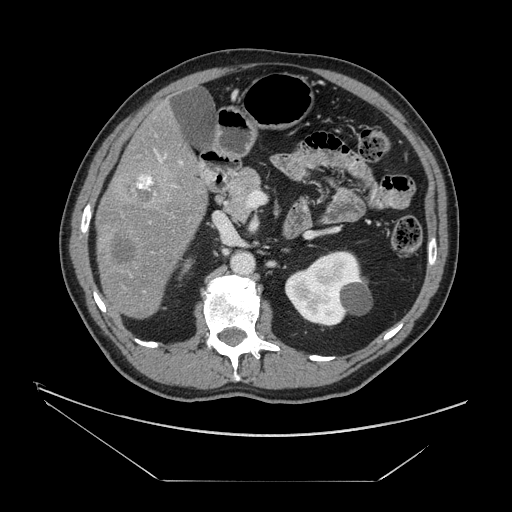
Contrast-enhanced abdominal CT, one axial slice; position 72 of 161 along the scan axis; 120 kVp; intravenous contrast given; soft-tissue window (W 400 / L 40 HU); 2.5 mm slice thickness; 512 × 512 image matrix, field of view 440 × 440 mm. Male patient, age 65 years. From the clinical record (not read from this slice): diagnosis: colorectal cancer liver metastases, imaged before liver resection; multiple liver metastases: yes; largest metastasis: 4.2 cm; chemotherapy before resection: yes.
Annotated regions visible in this slice (outlined manually by an expert reader):
- liver: box from (x=98, y=108) to (x=207, y=318) px
- portal vein (with intrahepatic branches): (x=138, y=156)–(x=181, y=195)
- liver metastasis: (x=114, y=239)–(x=139, y=266)
- liver metastasis: (x=126, y=172)–(x=160, y=203)